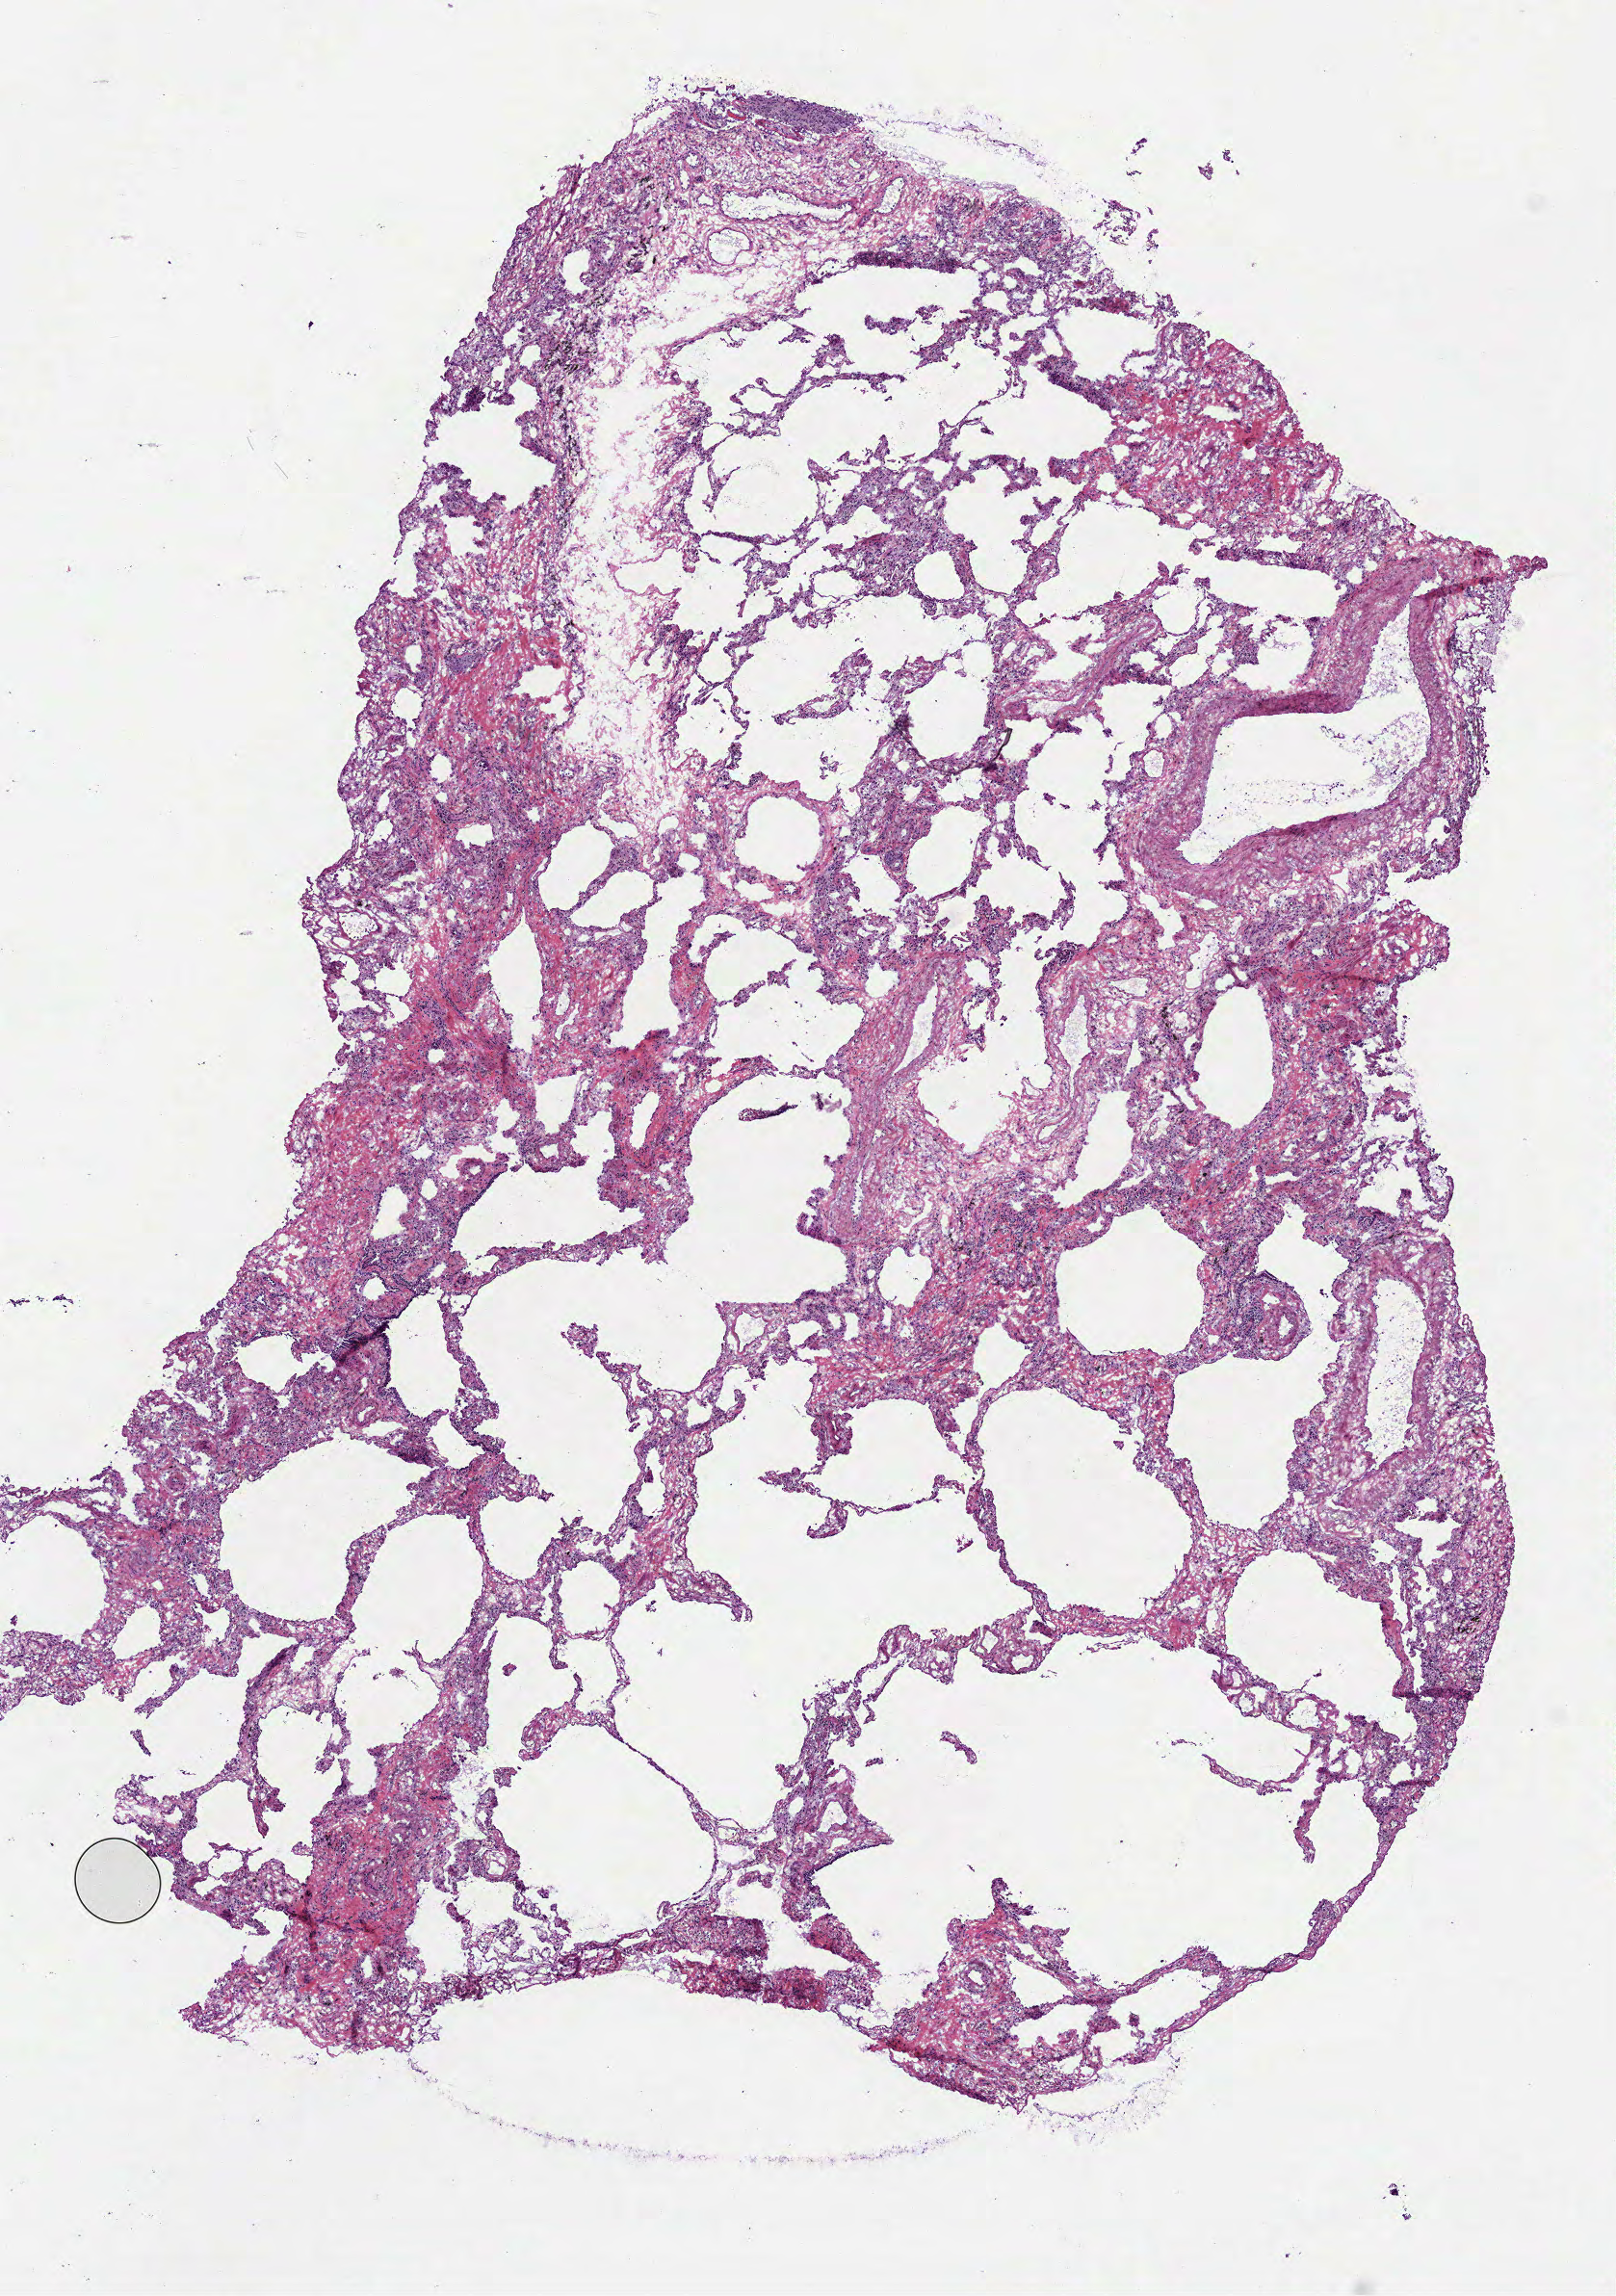
Hematoxylin and eosin (H&E) stained whole-slide image — shown as a low-resolution overview of the whole scanned area (about 6.8 x 9.6 mm, from a 40x scan). Frozen section from the top of the tissue portion. Sample: solid tissue normal (non-tumour tissue), lung. Male, age 77 years at initial diagnosis.
• this section: solid tissue normal (non-tumour) sample from the same patient
• patient diagnosis: Adenocarcinoma, NOS